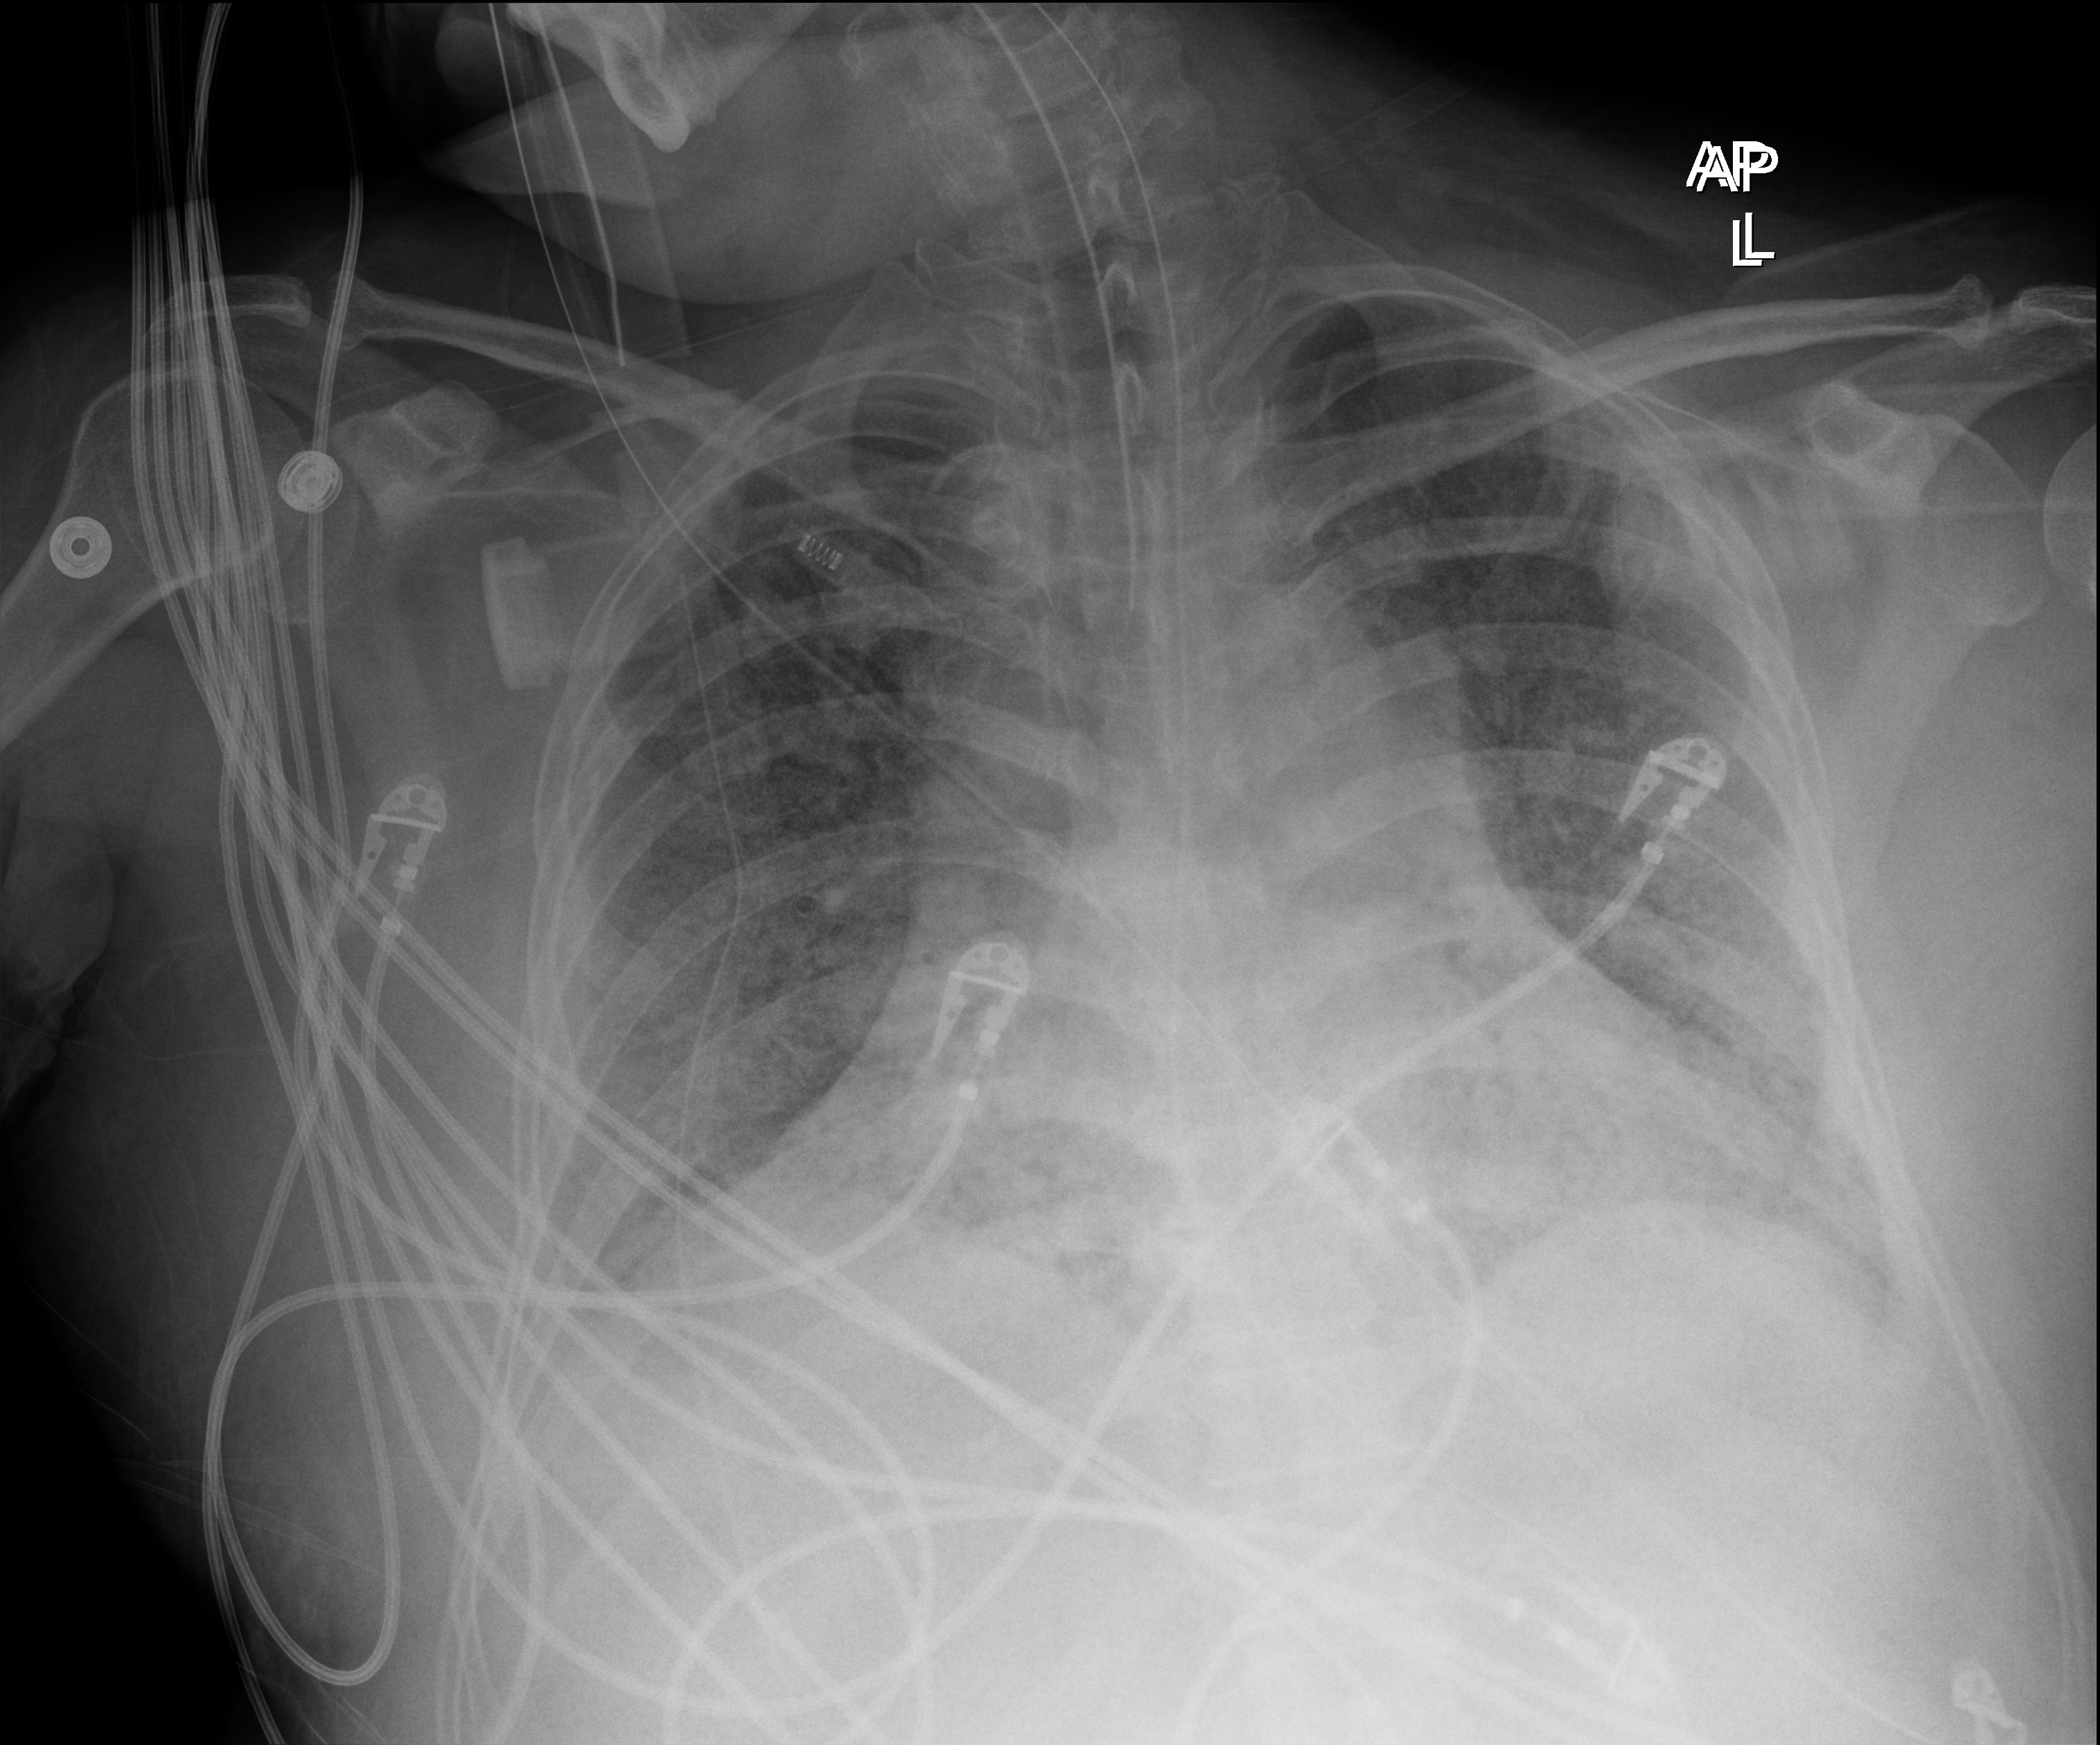
Chest X-ray (portable); anteroposterior (AP) projection. Adult patient hospitalised with COVID-19, age 18–59 years.
From the hospital-stay record, not from the radiograph (when in the stay this image was taken is not recorded):
- admitted to intensive care during this hospital stay: yes
- COPD (admission record): no
- mechanically ventilated during this hospital stay: yes